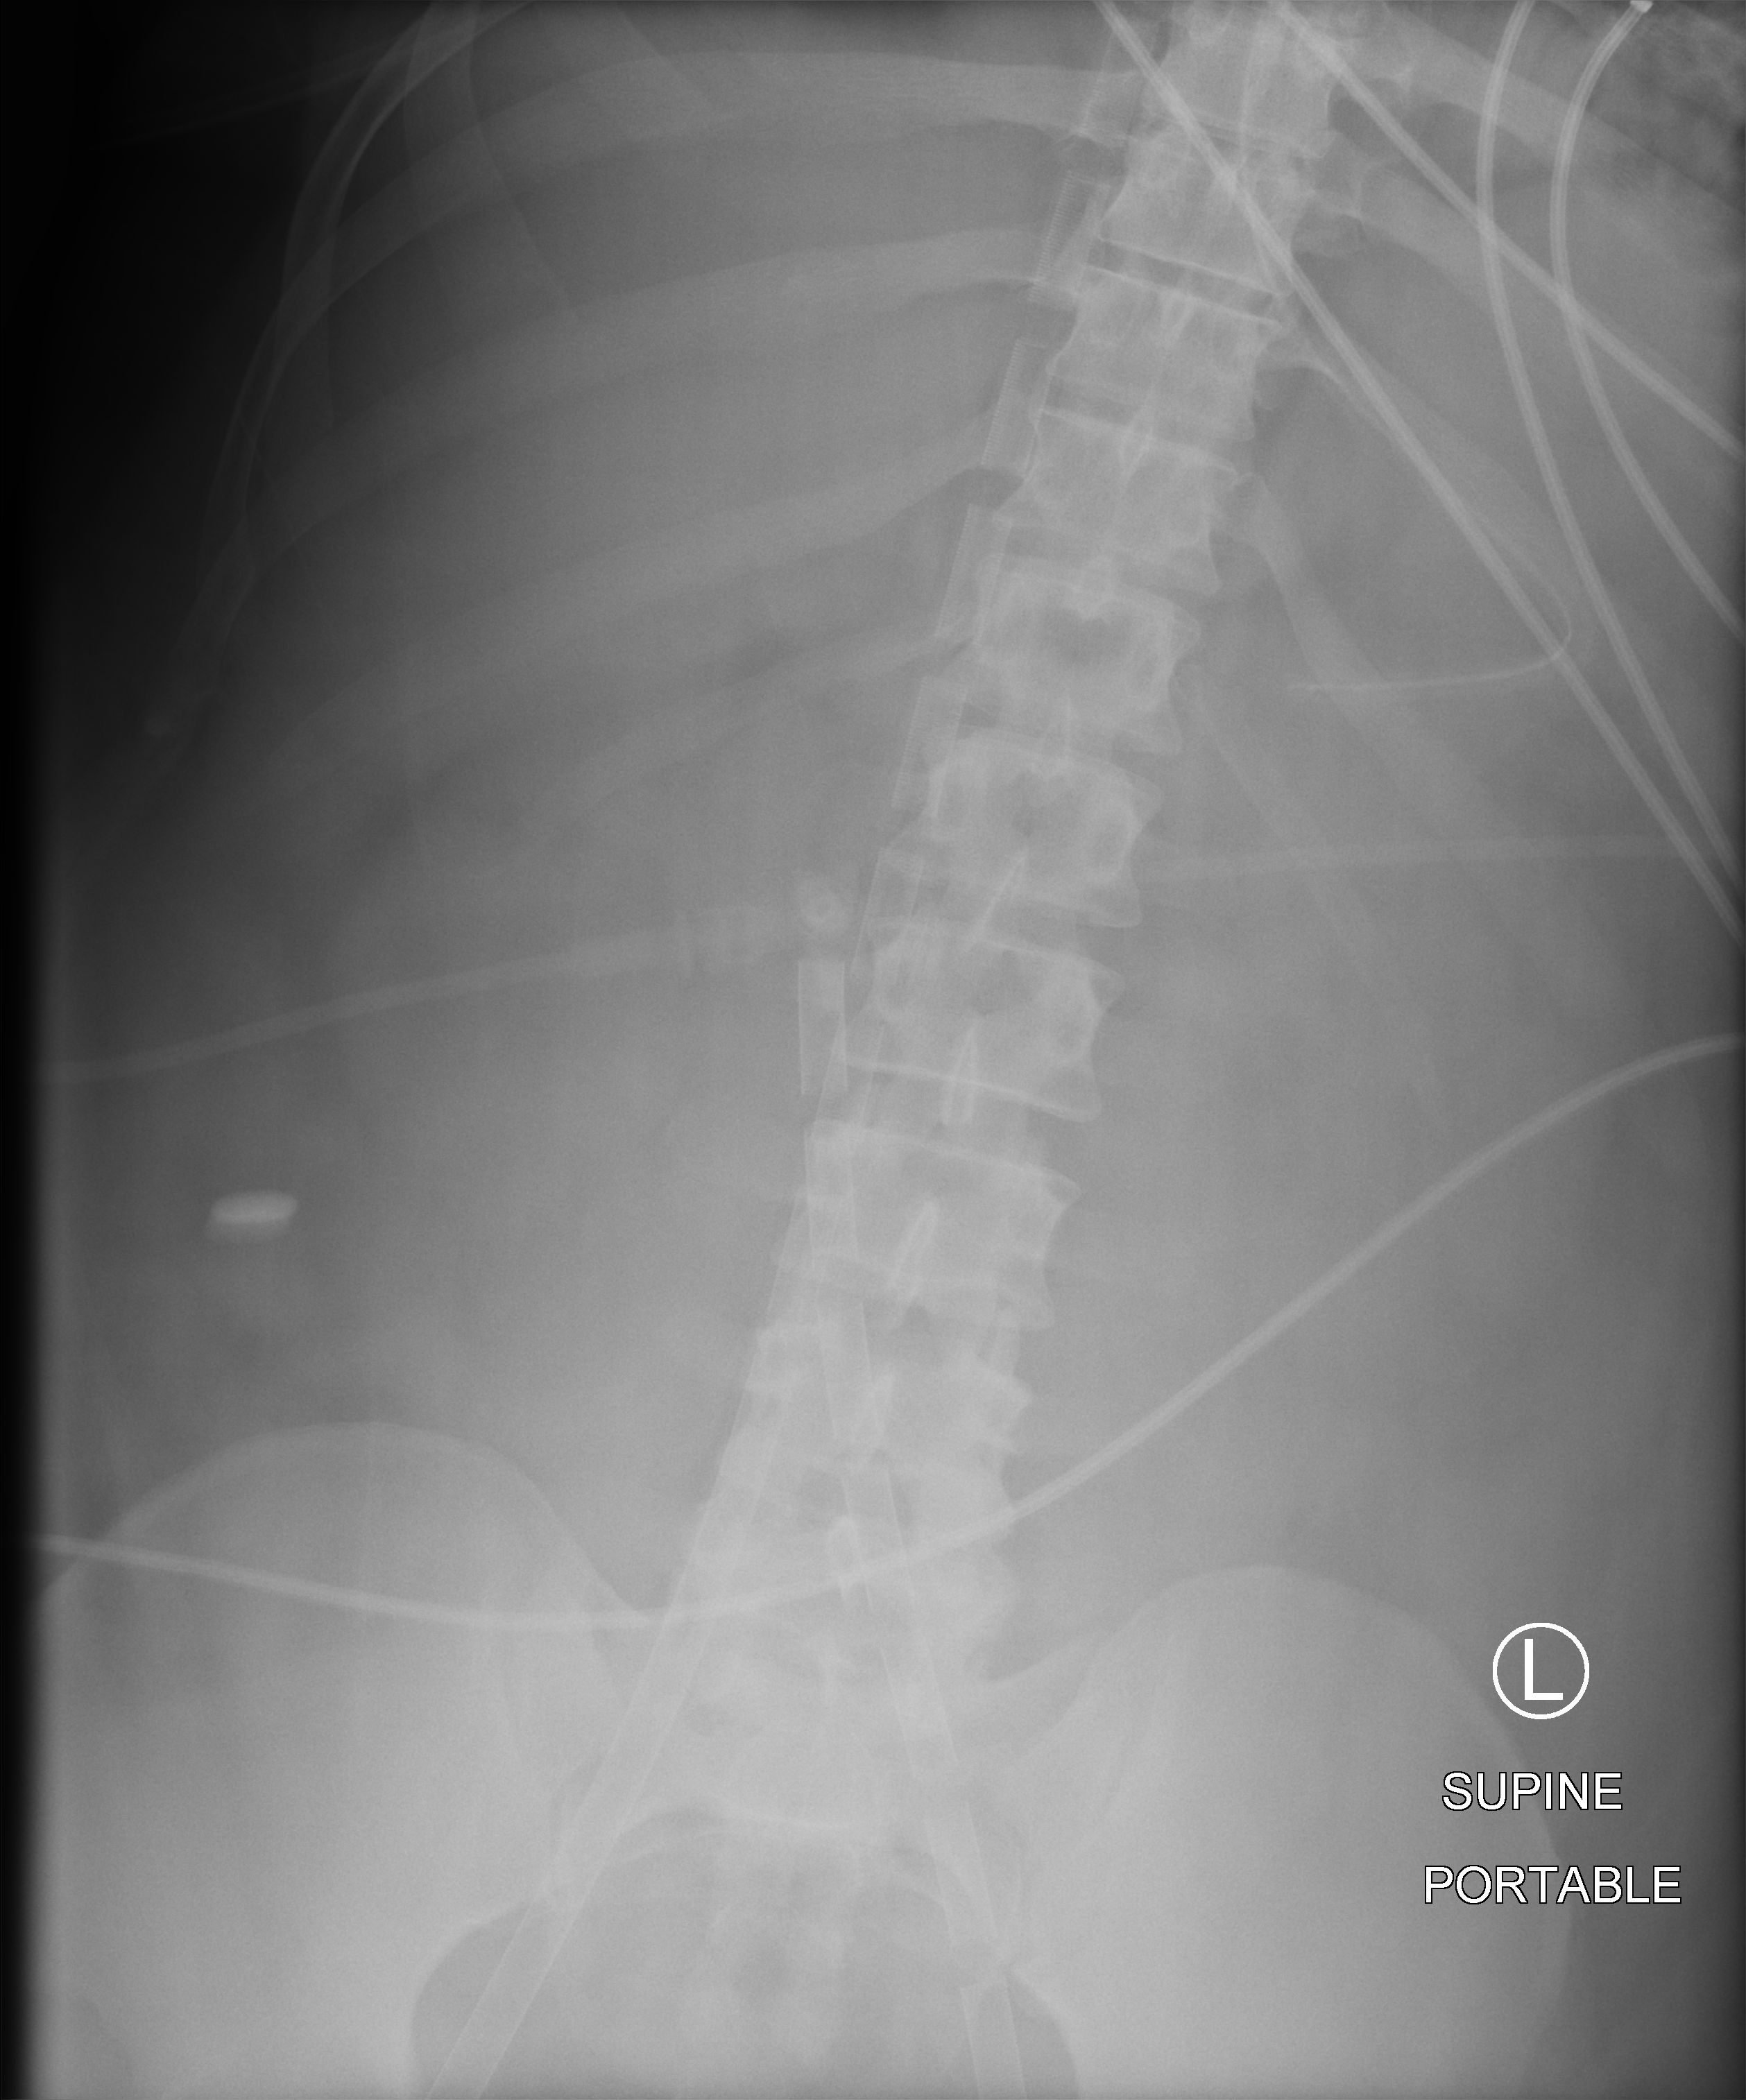
Bedside abdomen radiograph (computed radiography); anteroposterior (AP) projection. Adult patient hospitalised with COVID-19, age 18–59 years.
Hospital-stay facts (about this admission, not read from this image; timing relative to this image not recorded): COPD (admission record): no; mechanically ventilated during this hospital stay: yes; other chronic lung disease (admission record): no.